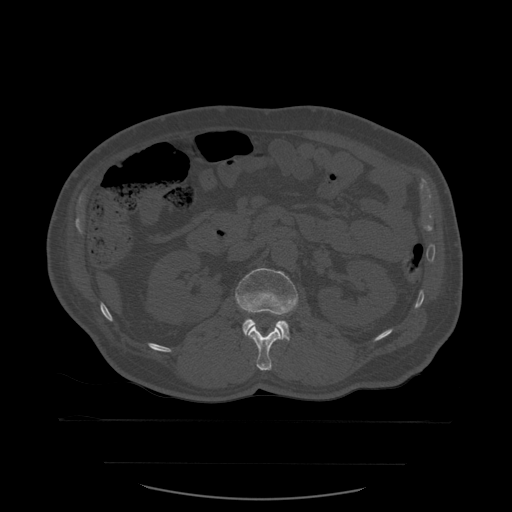
CT including the spine, one axial slice. Slice 232 of 590 in the series (ordered by position). Bone window (W 1800 / L 400 HU). 512 × 512 image matrix. Patient age 71 years. Case-level facts recorded for this patient, not image findings: primary cancer: lung; vertebrae with lytic lesions (as recorded): T1, T2, L5, S1.
Structures marked on this image (semi-automatic segmentation, software-assisted and operator-edited):
- L1 vertebra: bounding box [x1, y1, x2, y2] px = [248, 325, 282, 371]
- L2 vertebra: [235, 268, 299, 341]